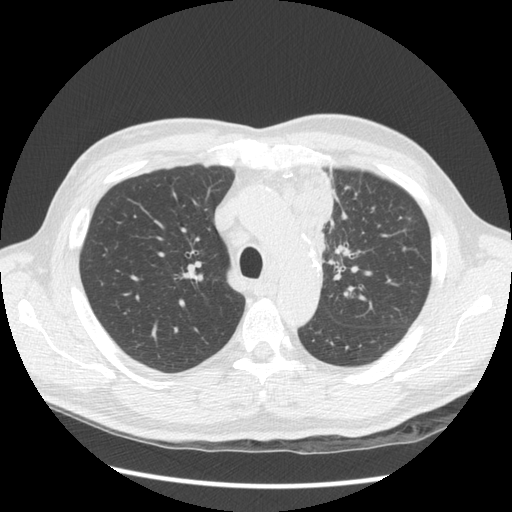
Low-dose screening chest CT, one axial slice; position 101 of 136 along the scan axis; 120 kVp; lung window (W 1500 / L -600 HU); 2.5 mm slice thickness; 512 × 512 image matrix.
Annotated regions visible in this slice (expert manual segmentation):
- lesion 1 (tumor, upper lobe of left lung): bounding box (x1, y1, x2, y2) in pixels: (297, 174, 333, 265)